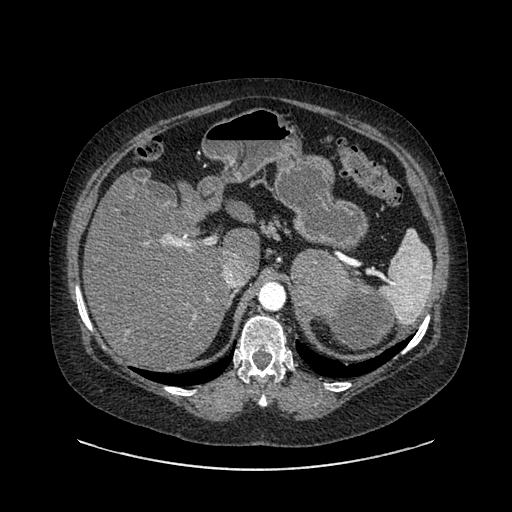
Contrast-enhanced abdominal CT, one axial slice. Slice 608 of 769 in the series (ordered by position). Reconstruction kernel SOFT. Intravenous contrast given. Soft-tissue window (W 400 / L 40 HU). 0.62 mm slice thickness. 512 × 512 image matrix, field of view 460 × 460 mm. Patient: female, 61 years. Case-level facts recorded for this patient, not image findings: diagnosis: adrenocortical carcinoma; tumour side: left adrenal; tumour size at pathology: 13 cm; Ki-67 index: 79 %; stage (as recorded): 2.
Structures marked on this image (semi-automatic segmentation, software-assisted and operator-edited):
- mass: bounding box <291,253,392,349> (left, top, right, bottom; pixels)